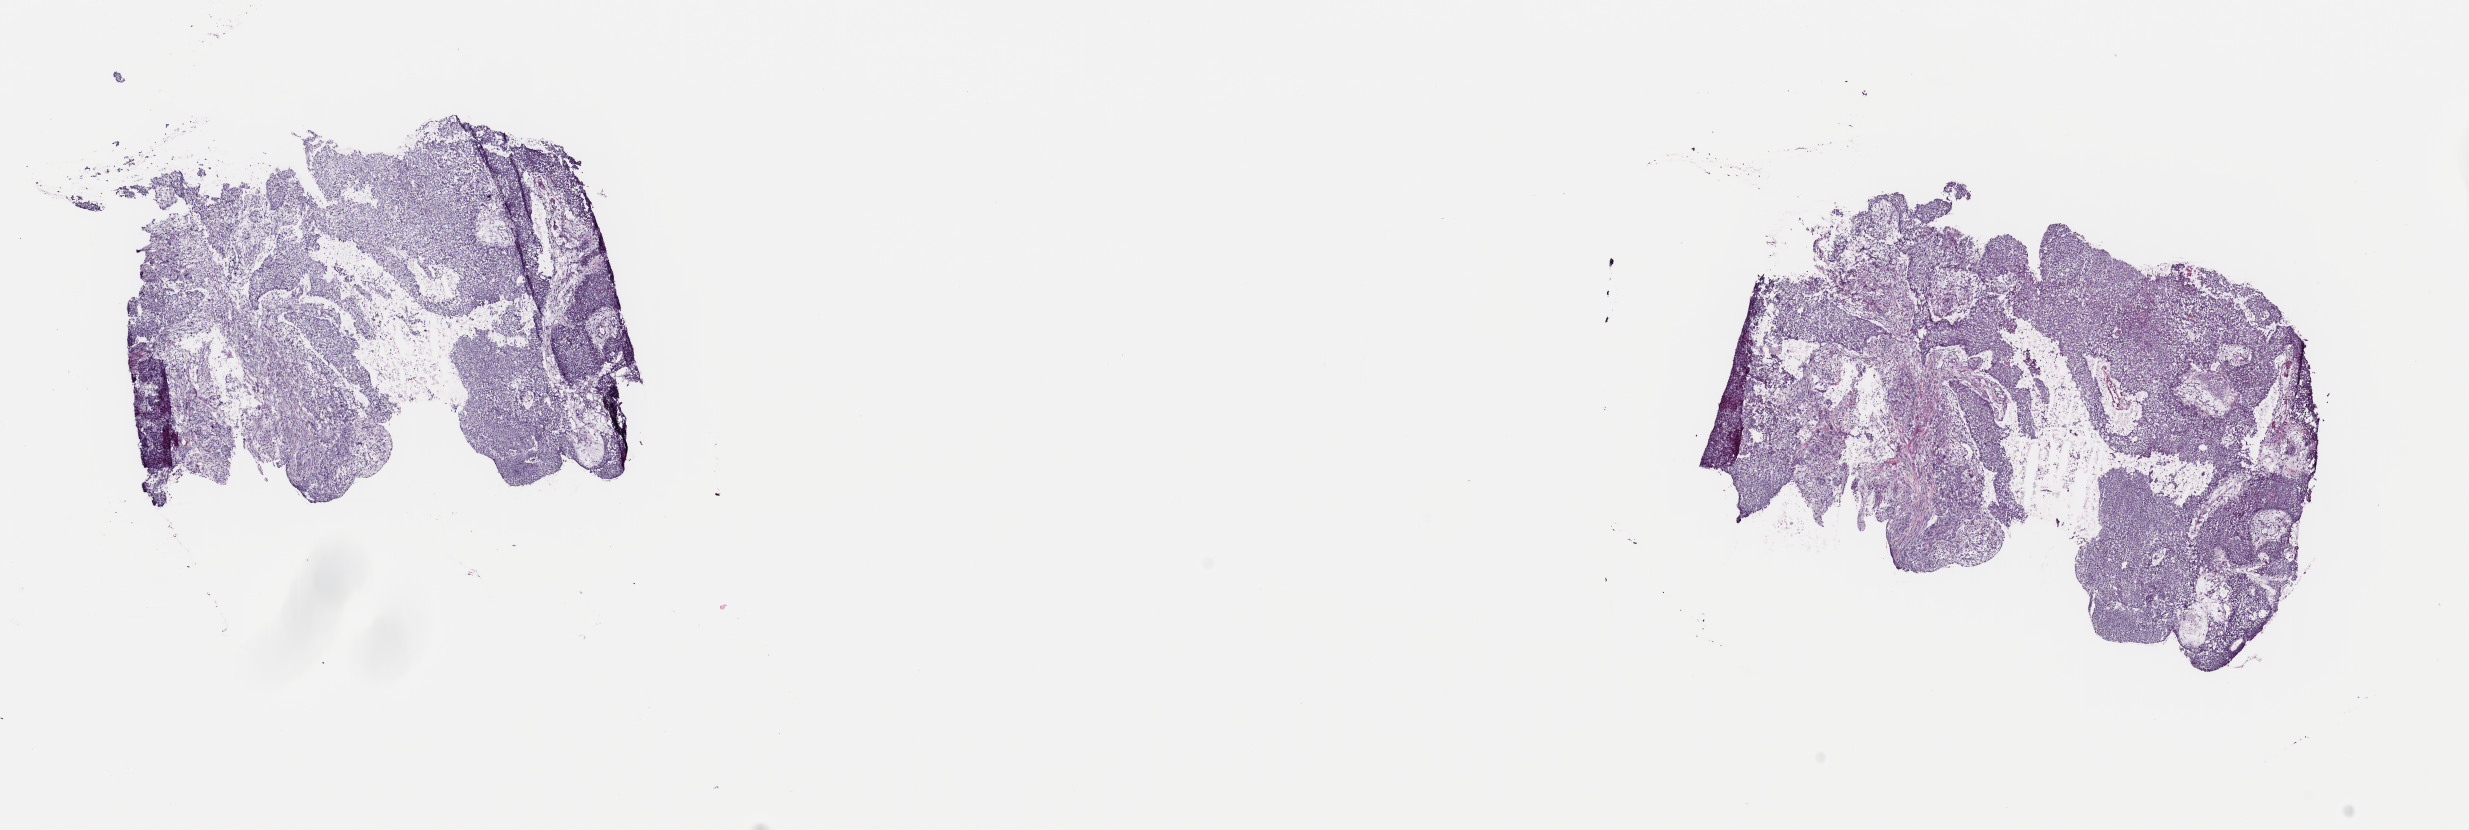
Digitized H&E tissue section (whole slide), whole scanned area (about 19.5 x 6.6 mm) shown as a low-resolution overview, frozen section from the top of the tissue portion, primary tumour sample from the bladder. Male patient; age at initial diagnosis 48 years. Histologic grade: high grade. Composition of this section per pathologist review: tumour cells 100%, tumour nuclei 95%, normal cells 0%, stromal cells 0%, necrosis 0%. Inflammatory infiltration, as recorded: lymphocyte infiltration 1%, monocyte infiltration 0%, neutrophil infiltration 0%.
* AJCC pathologic stage: IV
* histologic diagnosis: Transitional cell carcinoma
* lymph nodes positive (case pathology): 1 of 15 examined